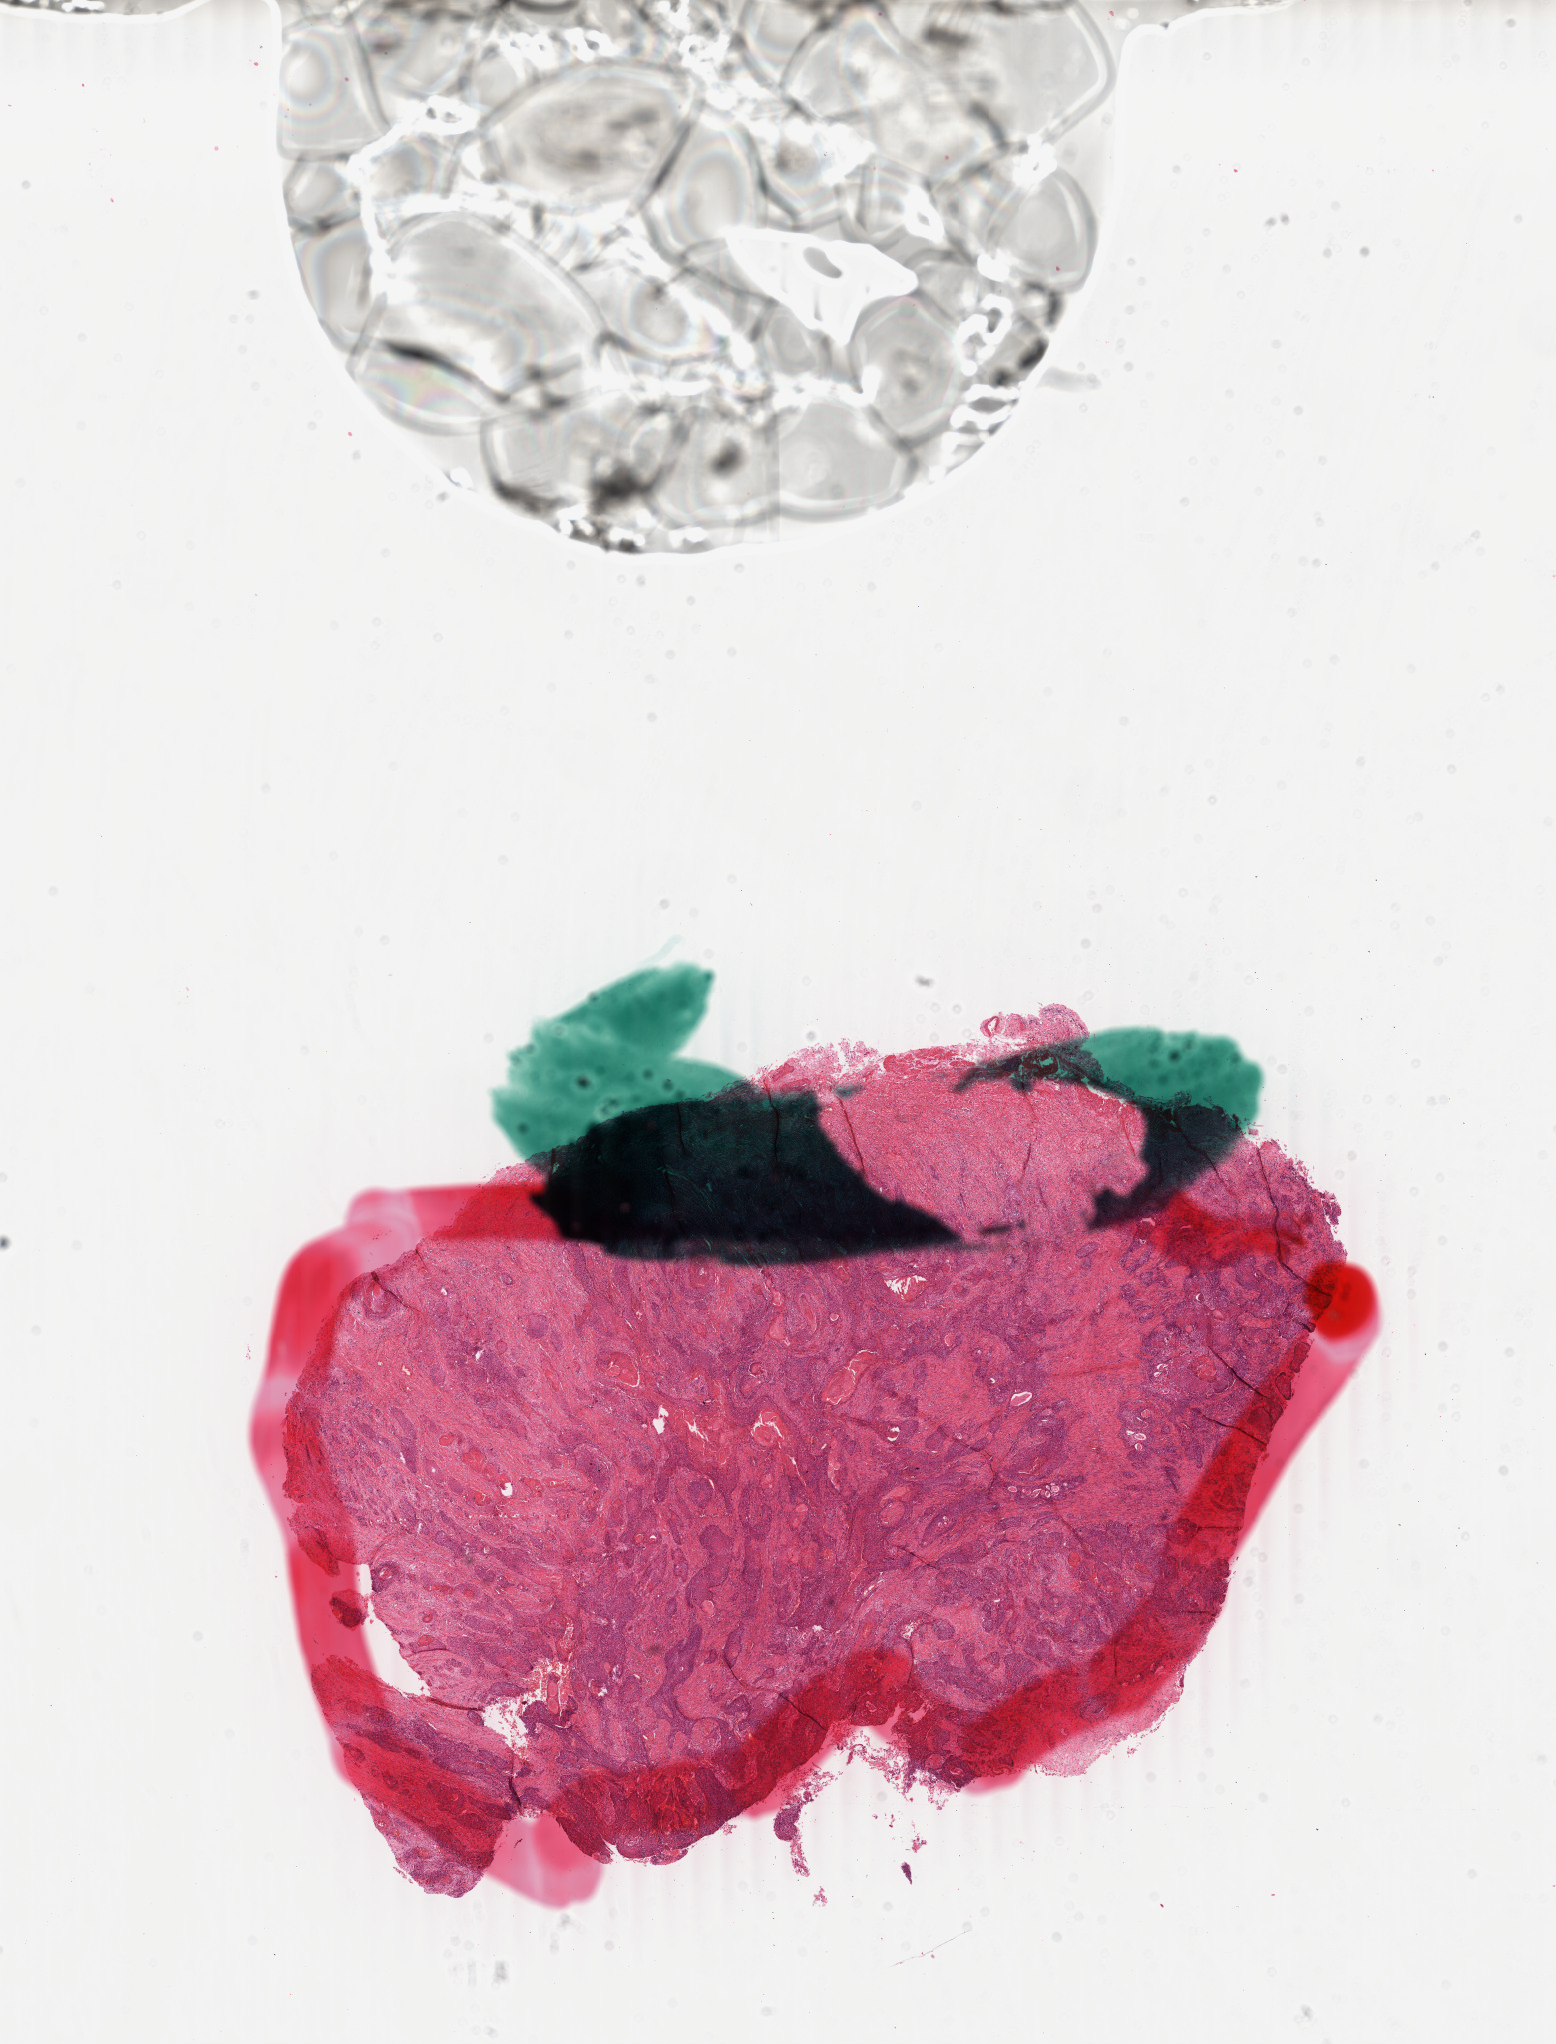
H&E whole-slide image, whole scanned area (about 12.4 x 16.3 mm, acquisition: 40x scan) shown as a low-resolution overview; formalin-fixed paraffin-embedded (FFPE) diagnostic section; primary tumour sample from the esophagus. Patient: male, age at initial diagnosis 58 years. Histologic grade: G2 (moderately differentiated).
Diagnosis: Squamous cell carcinoma, NOS (lower third of esophagus). AJCC pathologic stage: IIA (7th edition). Lymph nodes positive (case pathology): 0 of 4 examined.